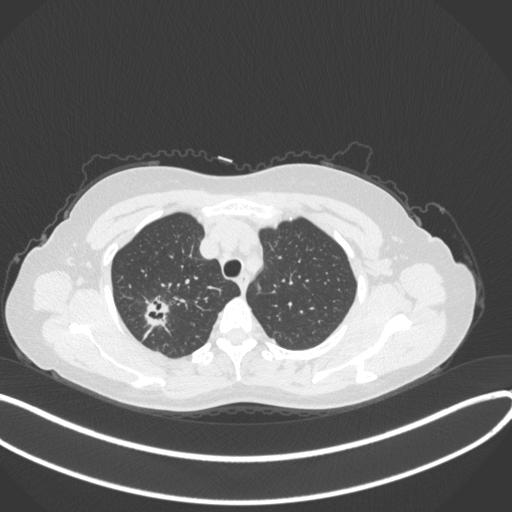
Chest CT, one axial slice. Position 294 of 342 along the scan axis. Reconstruction kernel B31f. 120 kVp. Lung window (W 1500 / L -600 HU). 1 mm slice thickness. 512 × 512 image matrix, field of view 400 × 400 mm. Female patient, age 50 years. Case-level facts recorded for this patient, not image findings: clinical TNM (as recorded): T1c N0 M0.
Structures marked on this image (bounding box drawn by a radiologist):
- lung tumour (recorded histology: adenocarcinoma): bounding box (x1, y1, x2, y2) in pixels: (141, 295, 169, 333)